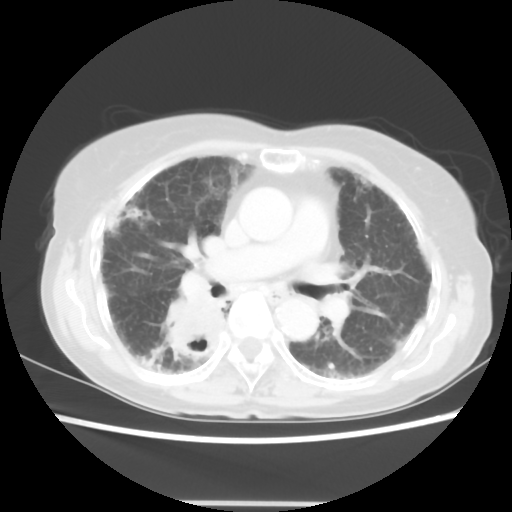
Chest CT, one axial slice. Position 30 of 52 along the scan axis. Lung window (W 1500 / L -600 HU). 512 × 512 image matrix, field of view 325 × 325 mm. Female patient, age 71 years. From the clinical record (not read from this slice): clinical TNM (as recorded): T3 N0 M0.
Outlined on this slice (rectangle marked by the reading radiologist):
- lung tumour (recorded histology: squamous cell carcinoma): box from (x=161, y=294) to (x=234, y=370) px